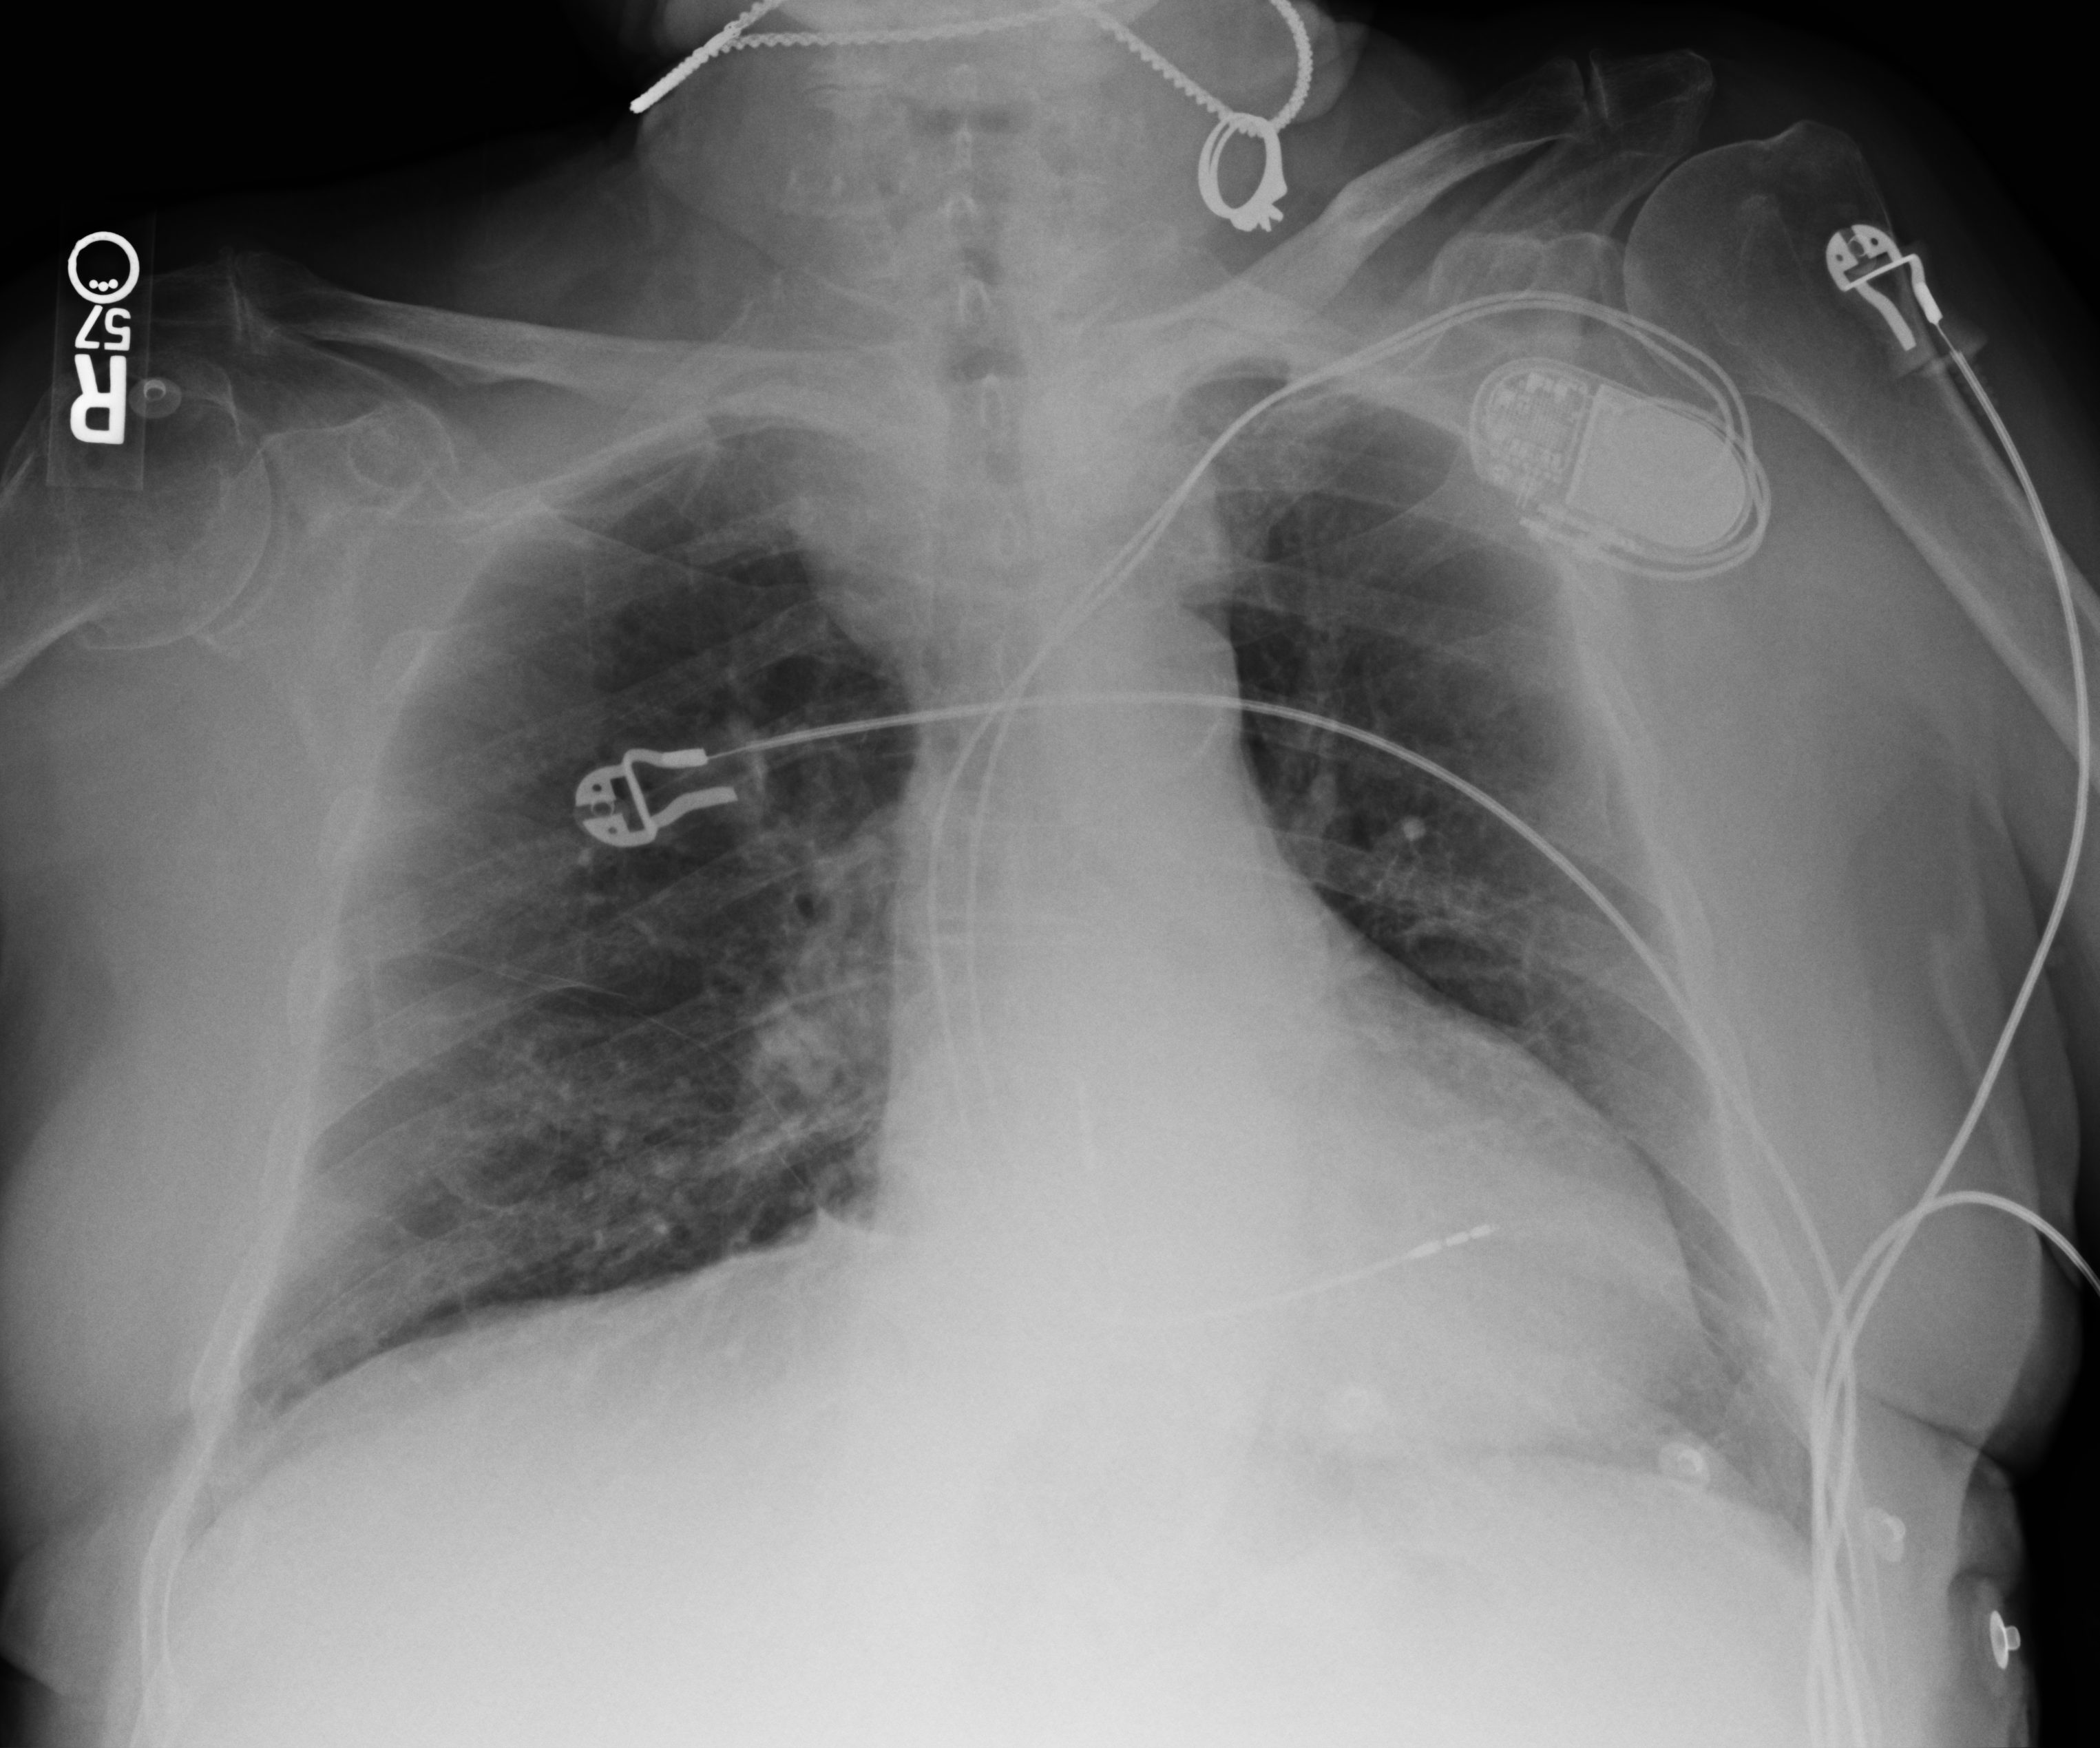
Chest X-ray (portable); anteroposterior (AP) projection. Patient hospitalised with COVID-19; male, aged 75–90 years.
From the hospital-stay record, not from the radiograph (when in the stay this image was taken is not recorded):
- mechanically ventilated during this hospital stay: no
- admitted to intensive care during this hospital stay: no